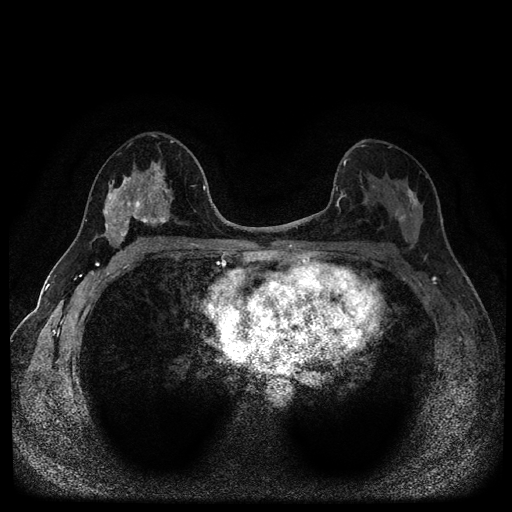
Breast MRI (dynamic contrast-enhanced, multi-phase), one axial slice. Position 56 of 116 along the scan axis. Dynamic contrast-enhanced series, time point 2 of 5 at this slice position (early post-contrast). 1.5 T. TE 2.7 ms, TR 5.4 ms. 2 mm slice thickness. 512 × 512 image matrix, field of view 320 × 320 mm. Patient: female, 49 years.
Structures marked on this image (semi-automatically segmented with operator editing):
- breast lesion (labelled benign in the annotation): bounding box <102,161,174,246> (left, top, right, bottom; pixels)